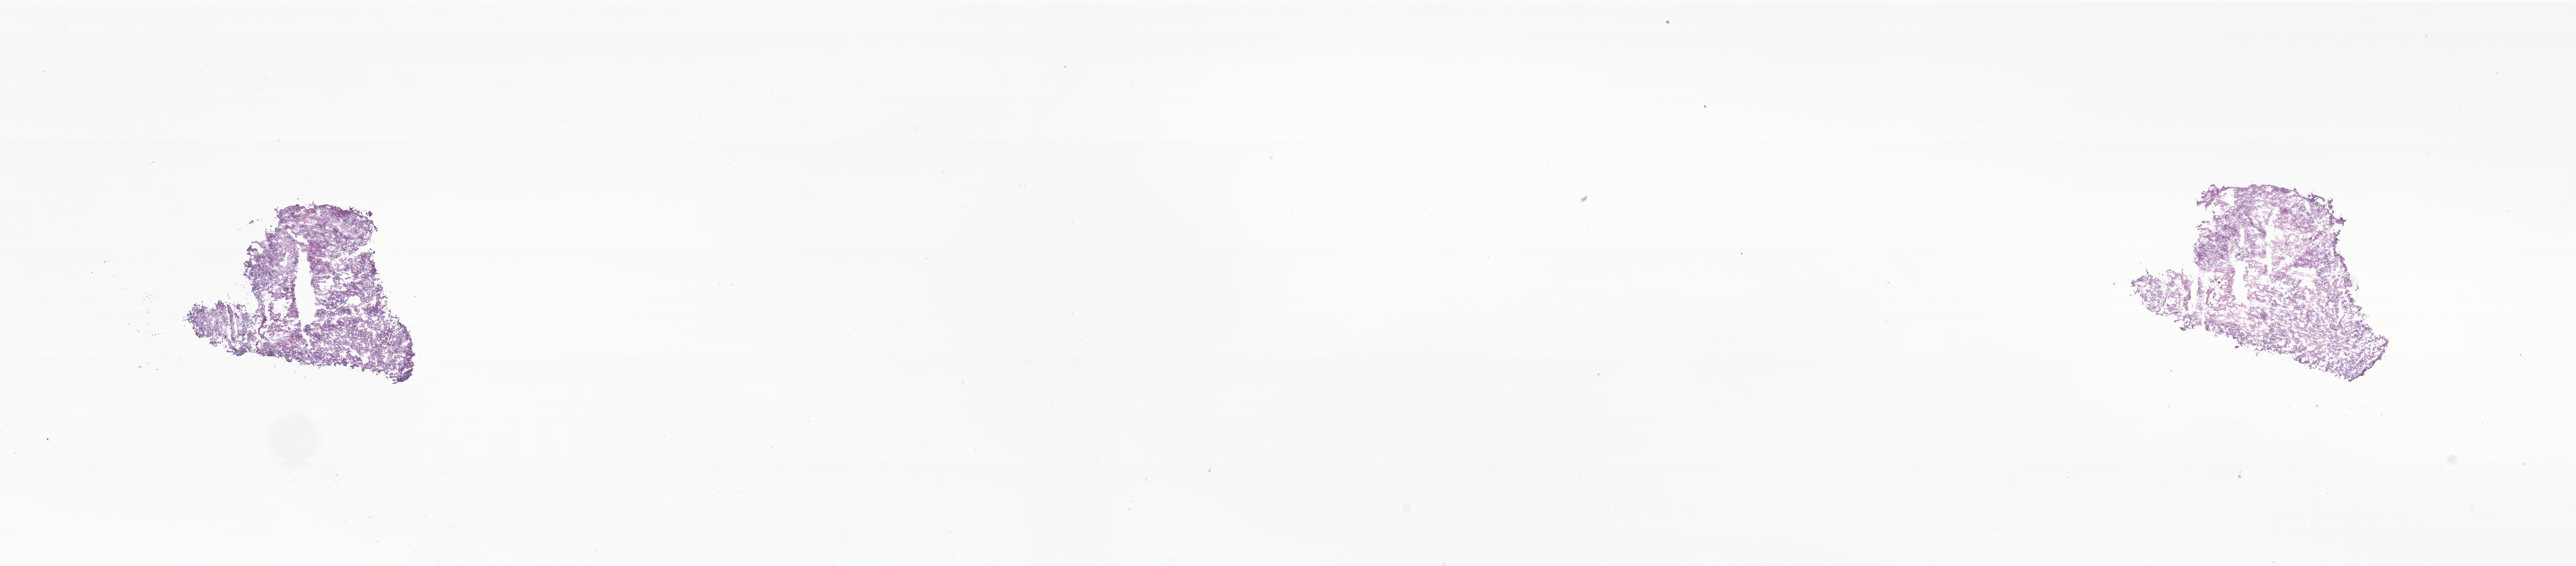
Whole-slide image, hematoxylin and eosin (H&E) stain of tumor tissue from the cerebellum, shown as a low-resolution overview of the whole scanned area (about 25.6 x 5.6 mm). Cryosection (OCT / tissue freezing medium). Male patient, age 74 months (6 years 2 months).
• recorded diagnosis: Ependymoma, NOS